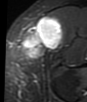
MRI of an extremity soft-tissue mass, one axial slice; slice 18 of 48 in the series (ordered by position); STIR; MR volume resampled by the dataset authors to the PET/CT grid (not the native acquisition matrix); 3.27 mm slice thickness; 87 × 102 image matrix, field of view 85 × 100 mm. Female patient. Case-level facts recorded for this patient, not image findings: histological type: synovial sarcoma; grade: intermediate; site of the primary tumour: right thigh.
Annotated regions visible in this slice (expert contour drawn on MRI and transferred to this co-registered scan by the dataset authors):
- gross tumour volume including surrounding oedema: bounding box (x1, y1, x2, y2) in pixels: (19, 18, 64, 57)
- gross tumour volume (mass): (19, 18, 64, 57)